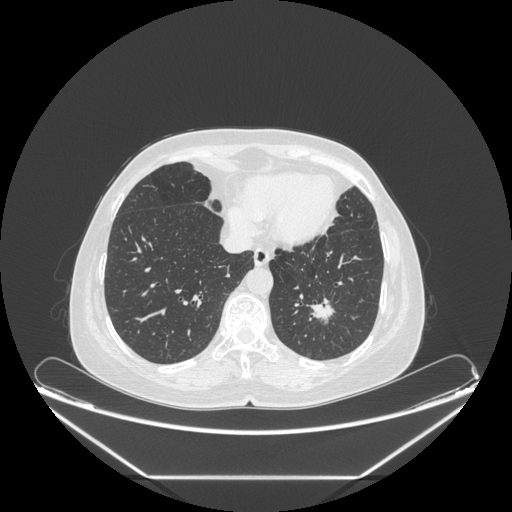
Chest CT, one axial slice; position 73 of 241 along the scan axis; reconstruction kernel STANDARD; 120 kVp; lung window (W 1500 / L -600 HU); 1.25 mm slice thickness; 512 × 512 image matrix. Patient: female, 63 years. Case-level facts recorded for this patient, not image findings: clinical TNM (as recorded): T1c N0 M0.
Outlined on this slice (rectangle marked by the reading radiologist):
- lung tumour (recorded histology: adenocarcinoma): bounding box [x1, y1, x2, y2] px = [310, 292, 339, 324]